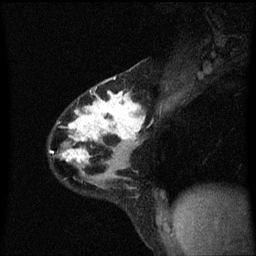
Breast MRI (dynamic contrast-enhanced), one sagittal slice. Slice 40 of 60 in the series (ordered by position). Dynamic contrast-enhanced series, image 2 of 3 at this slice position (ordered by acquisition). 1.5 T. TE 4.2 ms, TR 8.4 ms. 2 mm slice thickness. 256 × 256 image matrix. Female patient, age 32 years.
Outlined on this slice (semi-automatically segmented with operator editing):
- analysis volume of interest (the breast-tissue region the enhancement analysis was run in; not a lesion): bounding box [x1, y1, x2, y2] px = [49, 78, 146, 169]
- tumour enhancement mask (voxels above the 70 % enhancement threshold inside the analysis volume of interest): [50, 88, 145, 163]